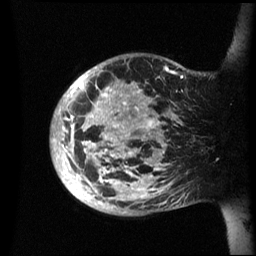
Breast MRI (dynamic contrast-enhanced), one sagittal slice; position 12 of 60 along the scan axis; dynamic contrast-enhanced series, image 2 of 3 at this slice position (ordered by acquisition); 1.5 T; TE 4.2 ms, TR 8.4 ms; 2.4 mm slice thickness; 256 × 256 image matrix. Patient: female, 48 years.
Outlined on this slice (semi-automatically segmented with operator editing):
- analysis volume of interest (the breast-tissue region the enhancement analysis was run in; not a lesion): bounding box (x1, y1, x2, y2) in pixels: (50, 53, 201, 216)
- tumour enhancement mask (voxels above the 70 % enhancement threshold inside the analysis volume of interest): (50, 67, 183, 198)